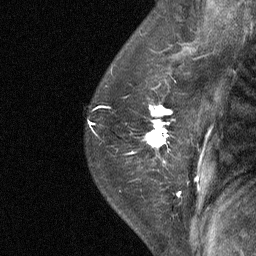
Breast MRI (dynamic contrast-enhanced), one sagittal slice; position 47 of 64 along the scan axis; dynamic contrast-enhanced study with each time point stored as its own series, time point 2 of 4 at this slice position (early post-contrast, ordered by acquisition time); 1.5 T; TE 4.8 ms, TR 27 ms; 2 mm slice thickness; 256 × 256 image matrix. Patient: female, 50 years. From the clinical record (not read from this slice): setting: breast cancer imaged before/during neoadjuvant chemotherapy; receptor status: HER2-positive.
Structures marked on this image (semi-automatically segmented with operator editing):
- analysis volume of interest (the breast-tissue region the enhancement analysis was run in; not a lesion): bounding box <123,91,189,177> (left, top, right, bottom; pixels)
- tumour enhancement mask (voxels above the 90 % enhancement threshold inside the analysis volume of interest): <145,105,171,148>